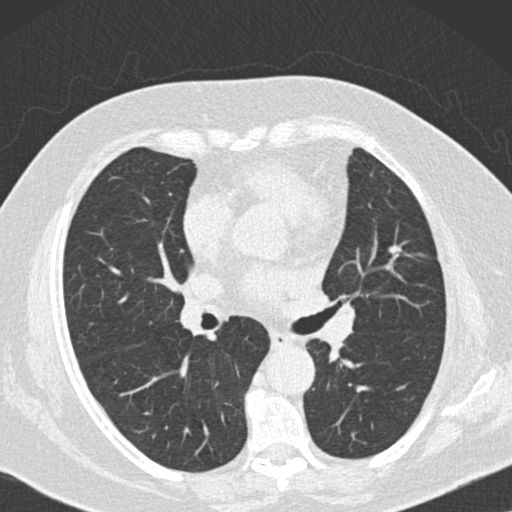
Chest CT (low-dose screening protocol), one axial image. Baseline annual screen. Lung window (W 1500 / L -600 HU). Slice 64 of 160 in the series. 512 × 512 image matrix, field of view 330 × 330 mm. Female participant, aged 73 years at enrolment. Current smoker at enrolment.
- Expert reader's lesion annotation, box from (x=373, y=232) to (x=417, y=273) px.
- Screening reader's record for this exam (one nodule recorded; not confirmed to be the boxed lesion): non-calcified nodule or mass ≥4 mm, right lower lobe, 7 × 7 mm, soft tissue attenuation.
- Note: the box lies in the patient's left hemithorax on this image, whereas the reader's record names the right lung; they may be different findings.
- Official screen result: positive, change unspecified: nodule(s) >= 4 mm or enlarging nodule(s), mass(es), or other non-specific abnormalities suspicious for lung cancer.